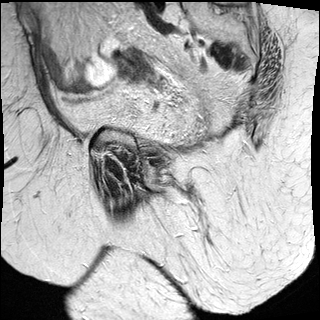
Pelvic MRI for cervical cancer, one sagittal slice. Slice 9 of 27 in the series (ordered by position). T2-weighted. 1.5 T. TE 89 ms, TR 2740 ms. 4 mm slice thickness. 320 × 320 image matrix, field of view 260 × 260 mm. Patient: female, 67 years.
Annotated regions visible in this slice (manually delineated by an expert):
- uterus and cervix: box from (x=117, y=48) to (x=156, y=85) px